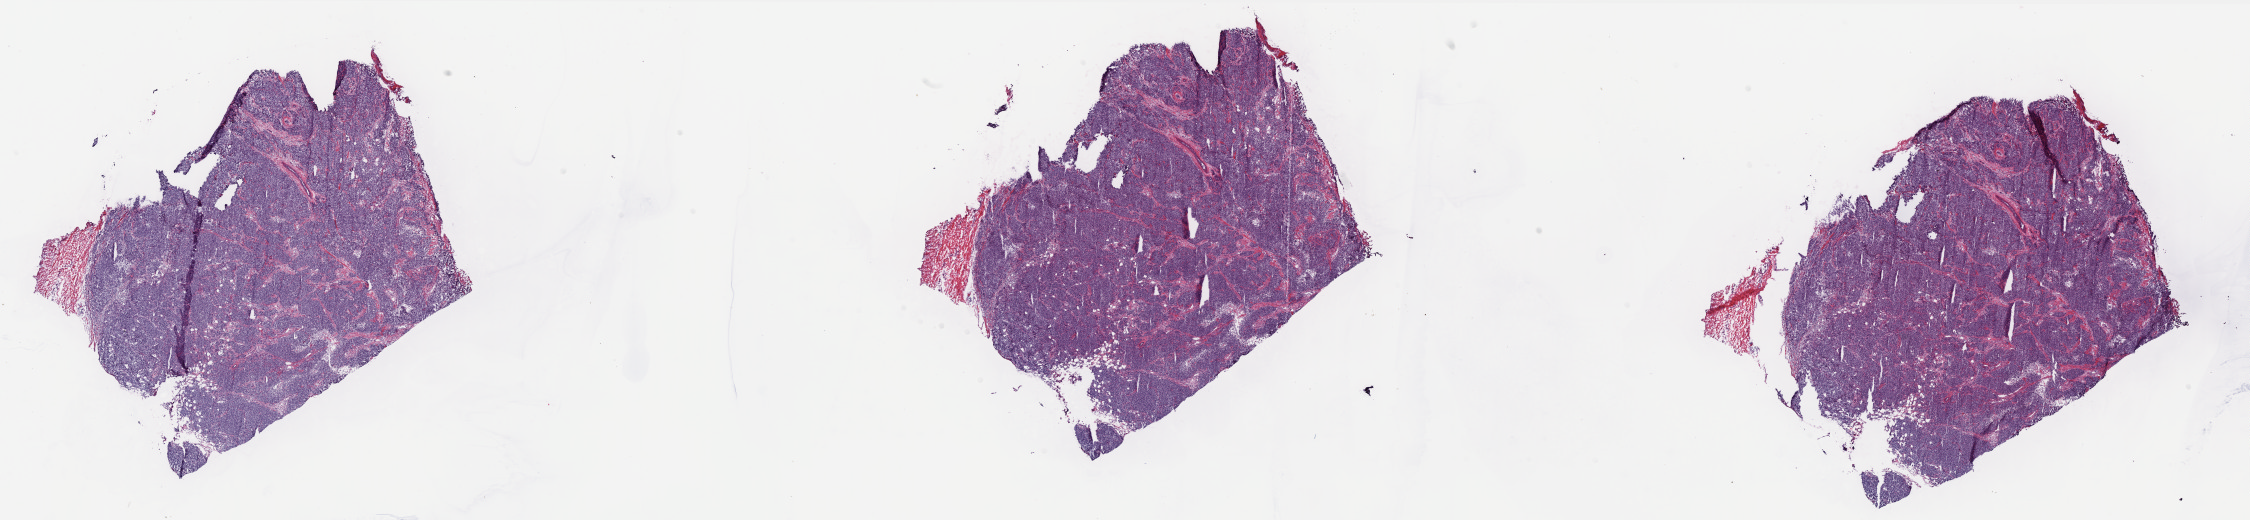
H&E whole-slide image, whole scanned area (about 36.1 x 8.3 mm) shown as a low-resolution overview, frozen section from the bottom of the tissue portion, sample: primary tumour, breast. Female patient; age at initial diagnosis 55 years. Slide review estimates, as recorded: tumour cells 80%, tumour nuclei 90%, normal cells 7%, stromal cells 10%, necrosis 3%. Infiltration values recorded for this section: lymphocyte infiltration 4%, monocyte infiltration 0%, neutrophil infiltration 0%.
• AJCC pathologic stage: IIA
• lymph nodes positive (case pathology): 0 of 17 examined
• pathologic diagnosis: Infiltrating duct carcinoma, NOS